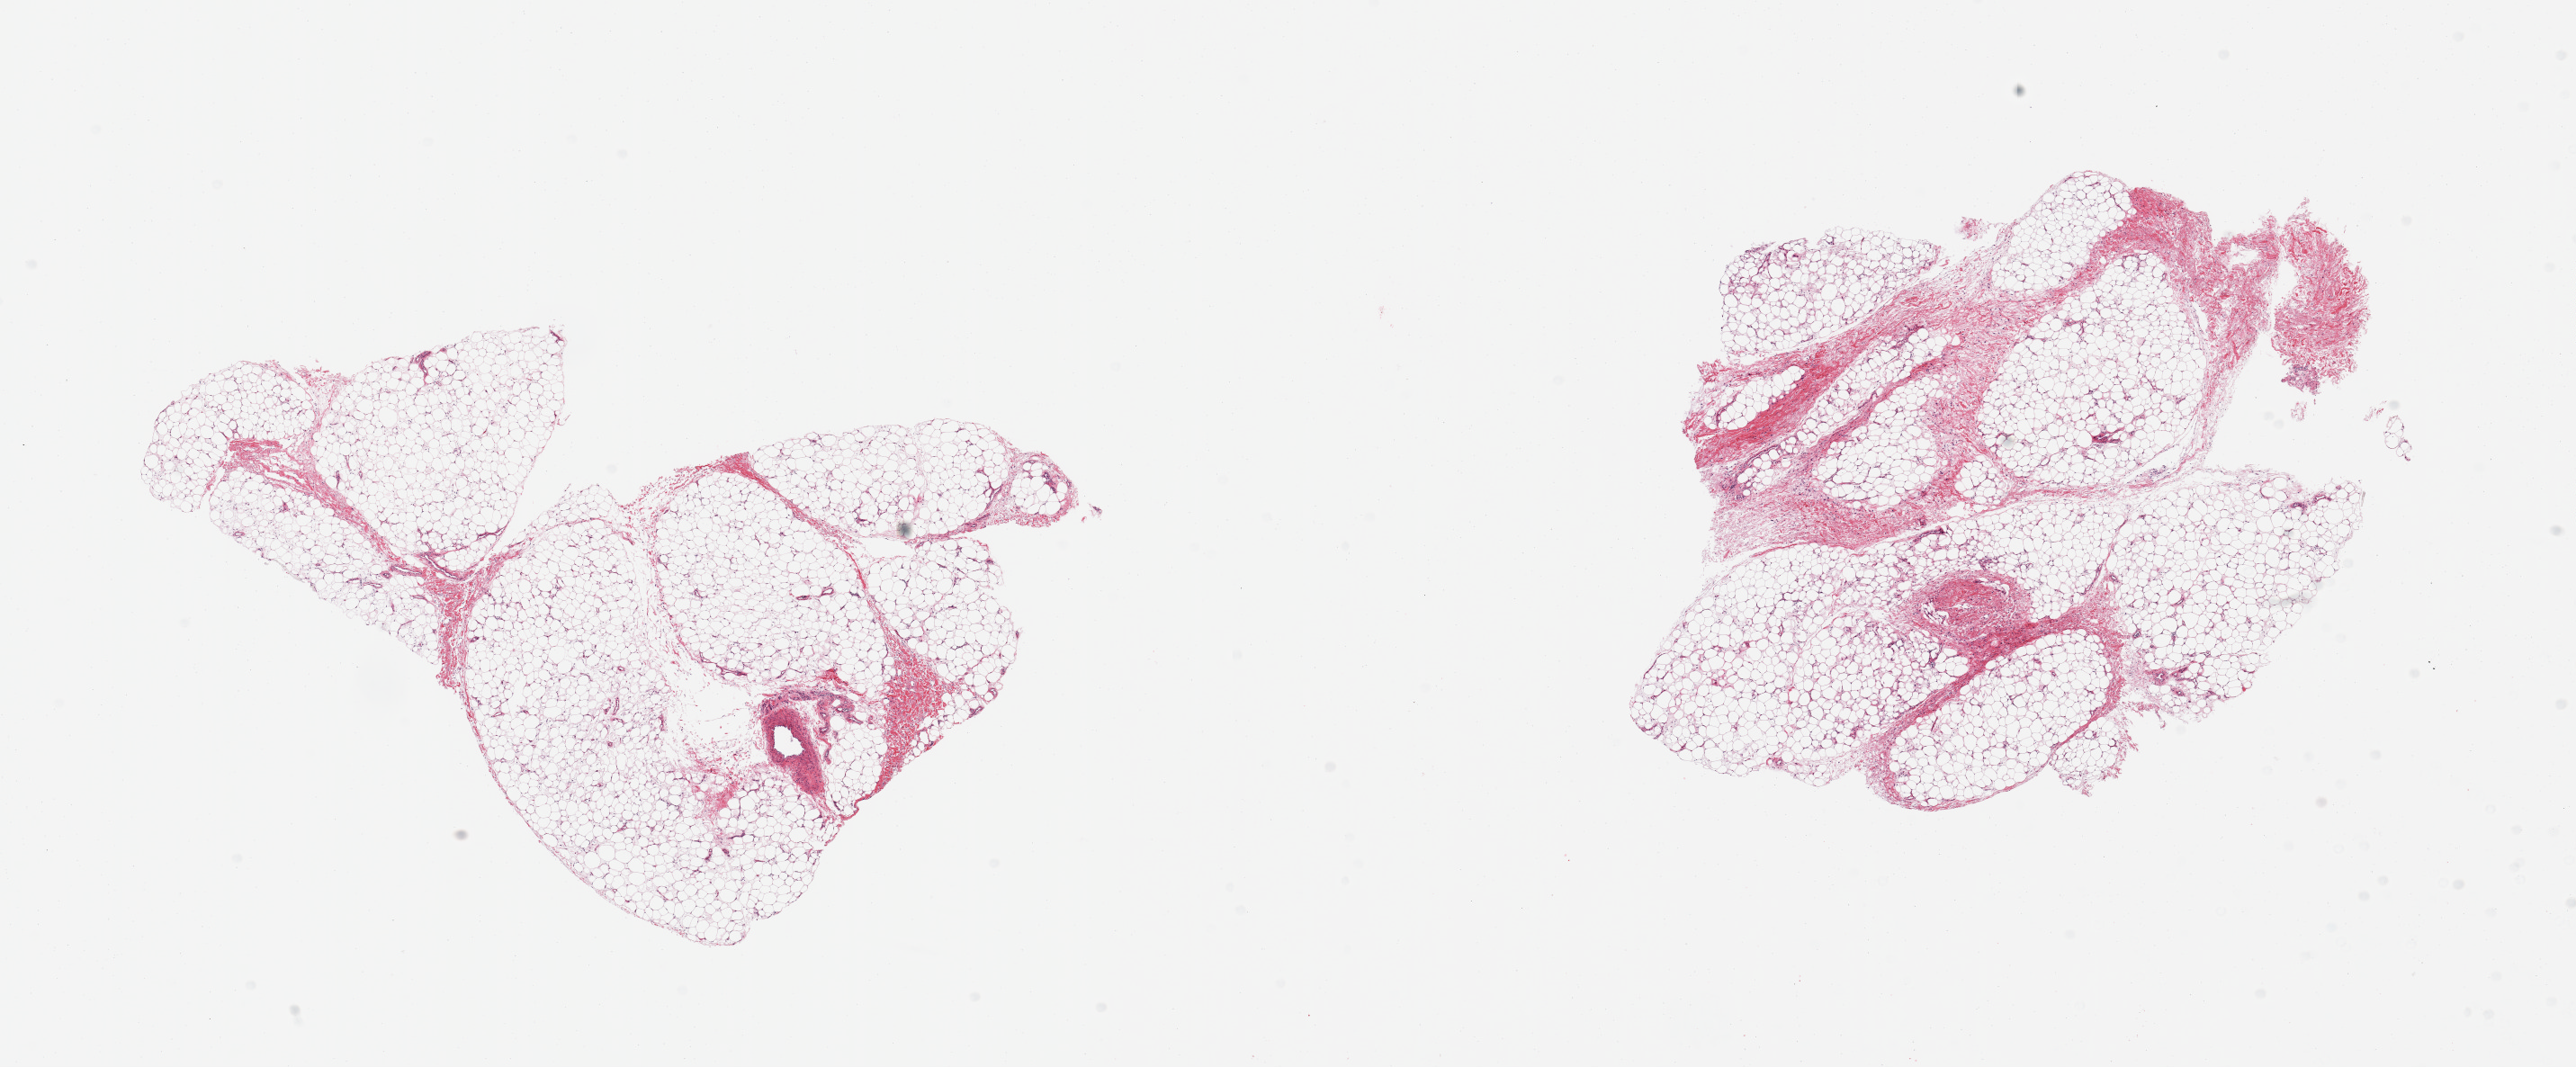
Whole-slide image, H&E stain, brightfield — low-resolution overview of the scanned area, about 22.6 x 9.4 mm (acquisition: 20x scan), PAXgene-fixed, paraffin-embedded tissue, sampled site (target tissue): adipose tissue, tissue donor sample. Male donor.
- pathologist's review note for this sample: 2 pieces; mature fat with up to 20% loose fibrous tissue